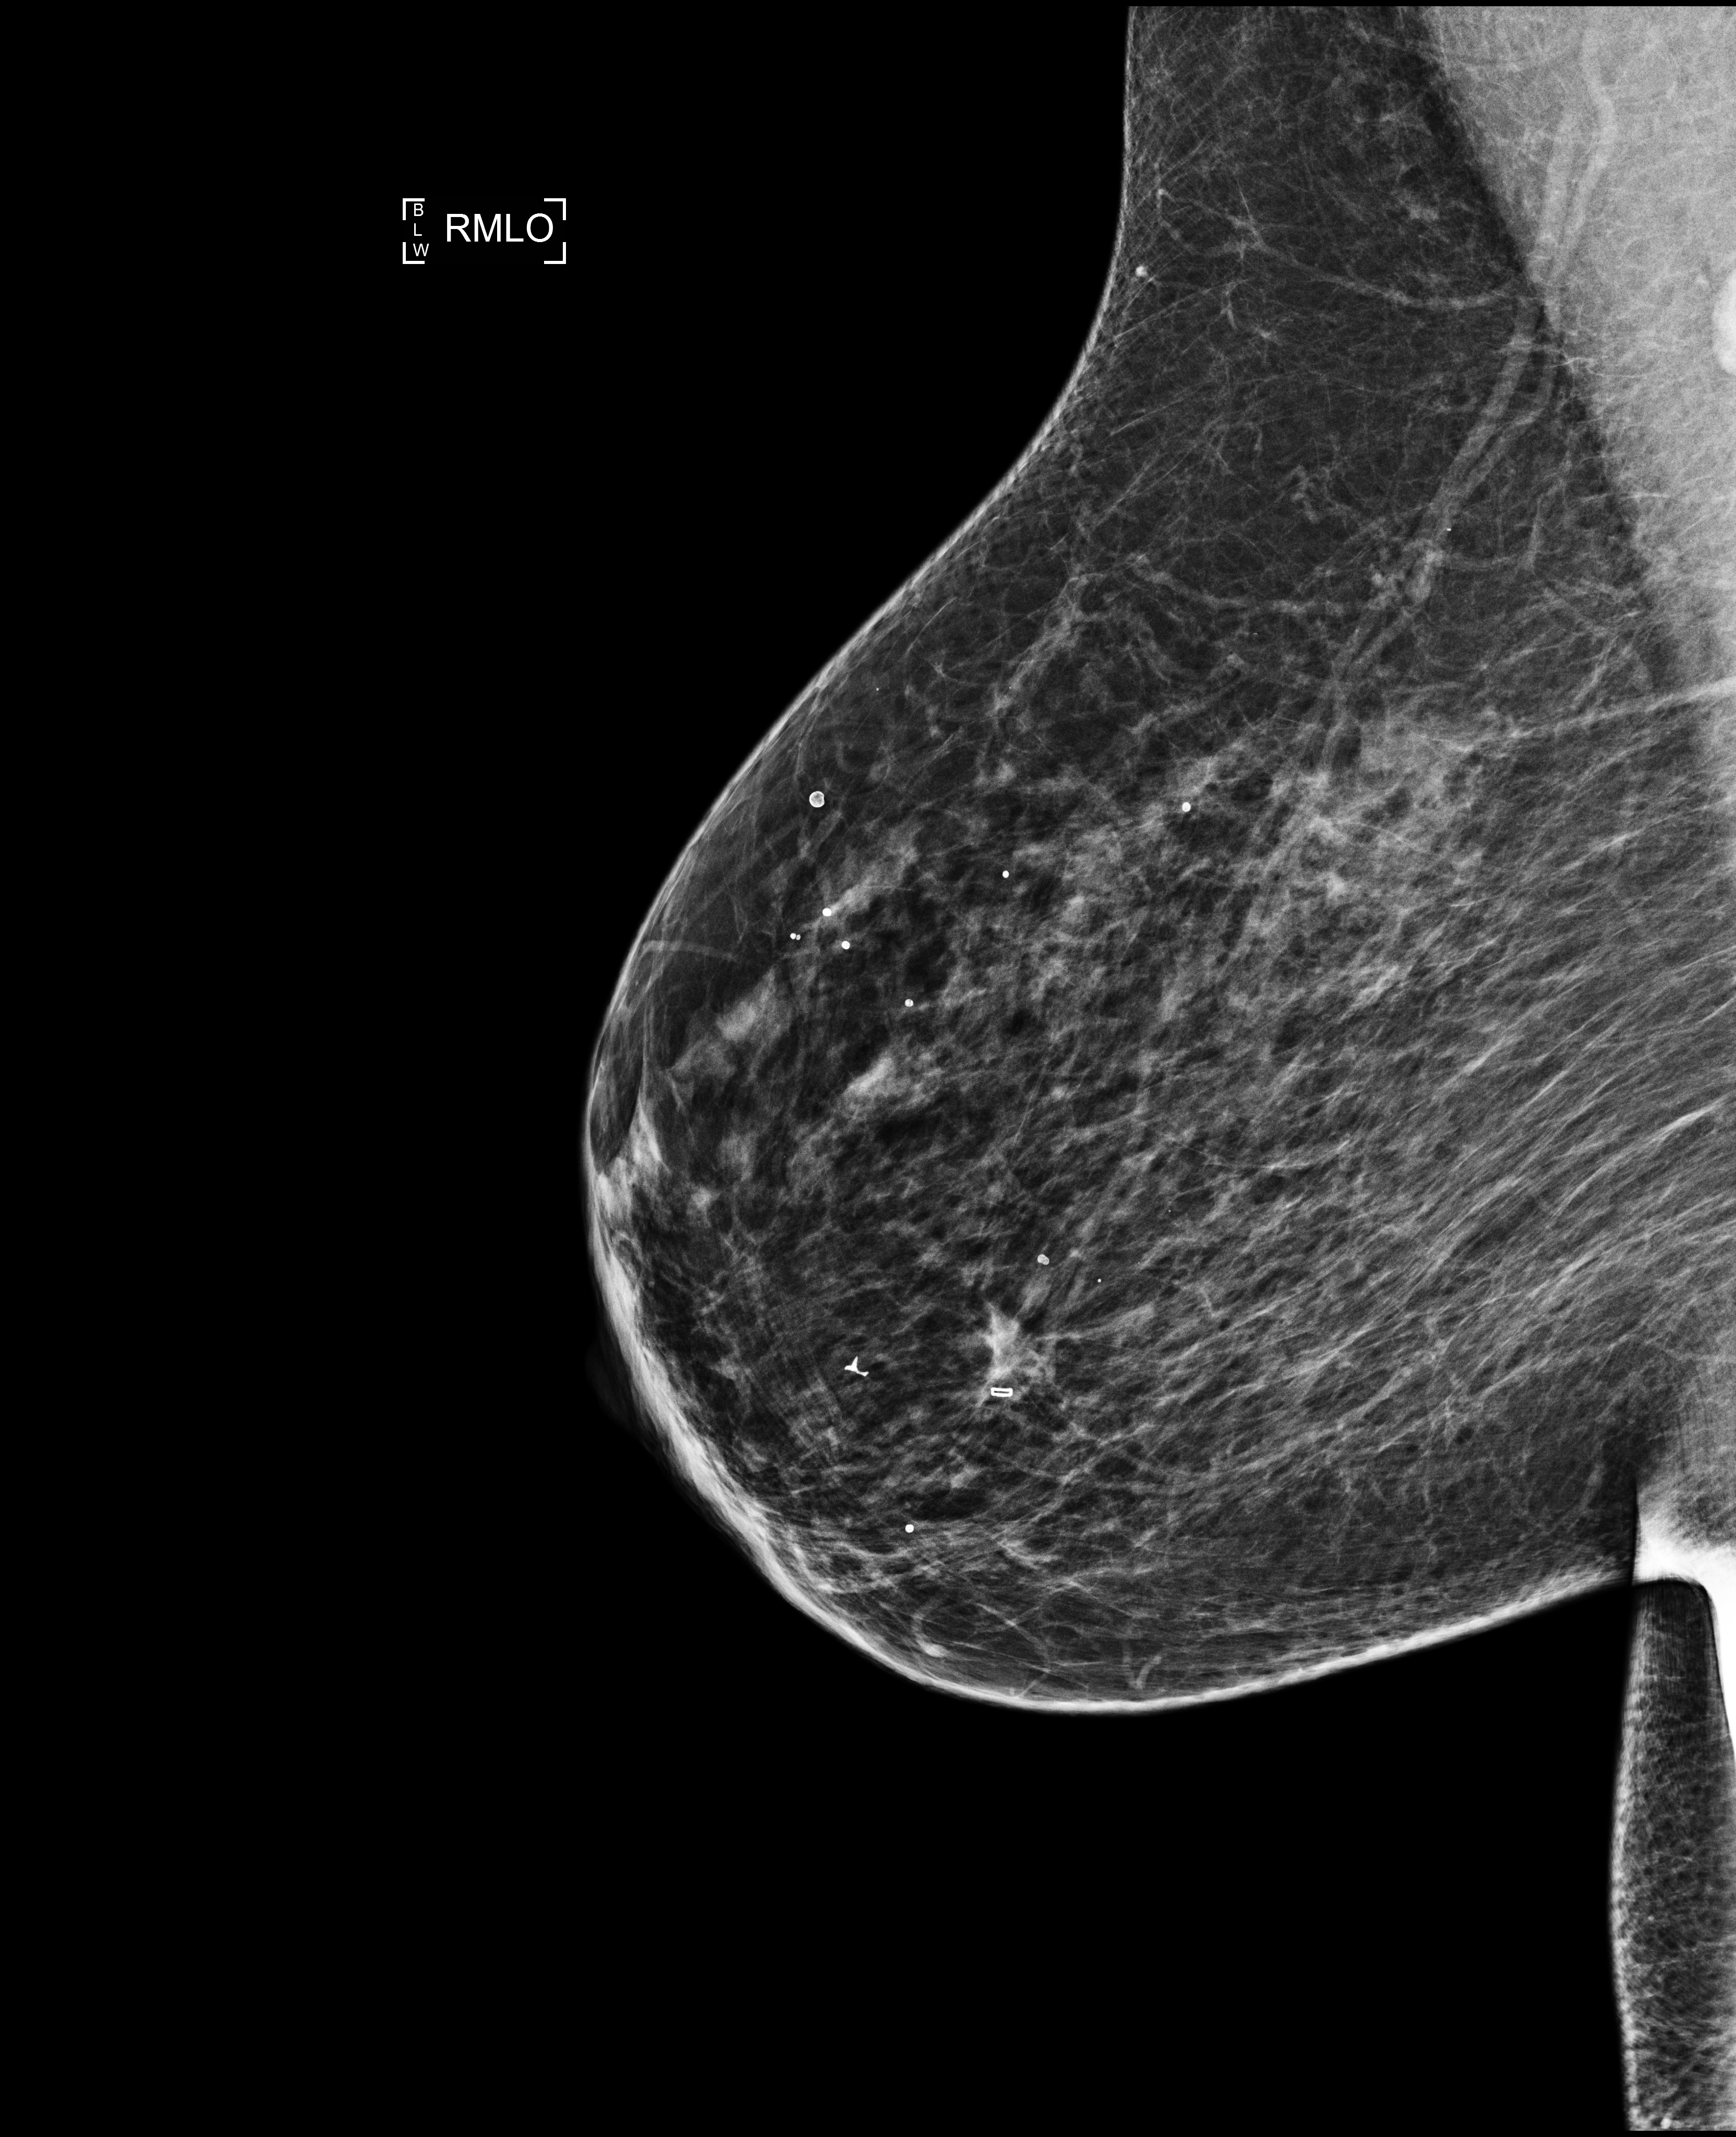
Screening examination, compressed breast thickness 44 mm. Female patient, age 69 years.
Image type: full-field digital mammogram. Breast: right. Projection: mediolateral oblique (MLO) view.